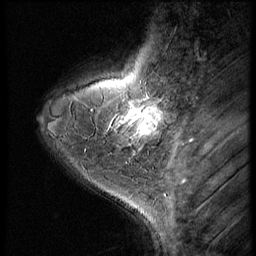
Breast MRI (dynamic contrast-enhanced), one sagittal slice. Slice 15 of 56 in the series (ordered by position). Dynamic contrast-enhanced series, image 2 of 3 at this slice position (ordered by acquisition). 1.5 T. TE 4.2 ms, TR 9 ms. 256 × 256 image matrix. Patient: female, 38 years. From the clinical record (not read from this slice): setting: breast cancer imaged before/during neoadjuvant chemotherapy; receptor status: triple-negative.
Annotated regions visible in this slice (semi-automatically segmented with operator editing):
- analysis volume of interest (the breast-tissue region the enhancement analysis was run in; not a lesion): bounding box (x1, y1, x2, y2) in pixels: (107, 95, 179, 149)
- tumour enhancement mask (voxels above the 140 % enhancement threshold inside the analysis volume of interest): (116, 102, 160, 135)